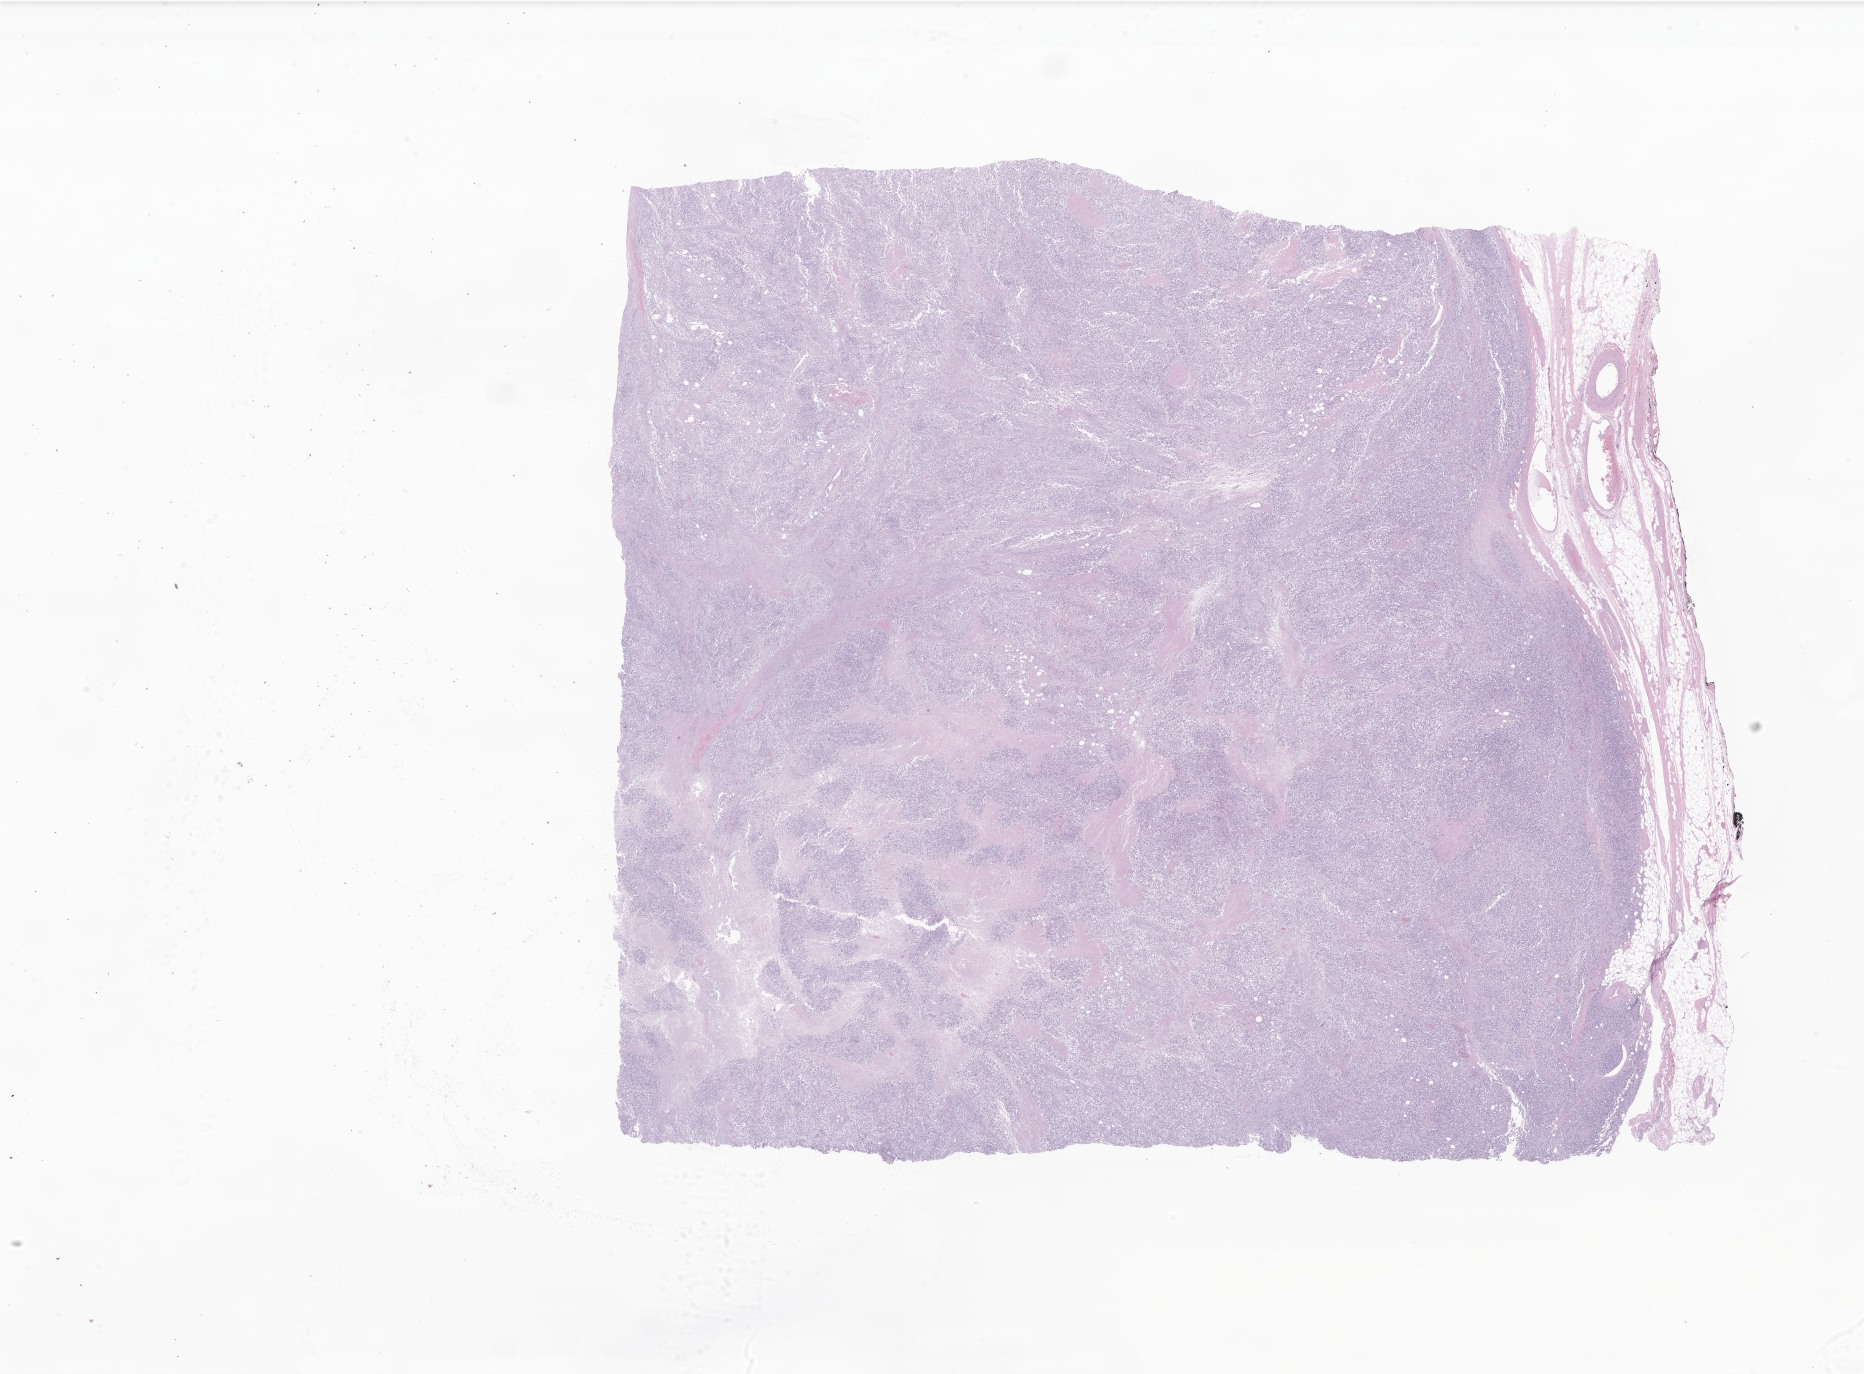
H&E whole-slide image of tumor tissue from the testis, low-resolution overview of the scanned area, about 31.4 x 23.2 mm; FFPE section. Patient male; age 177 months (14 years 9 months).
Diagnosis: Embryonal rhabdomyosarcoma, NOS.